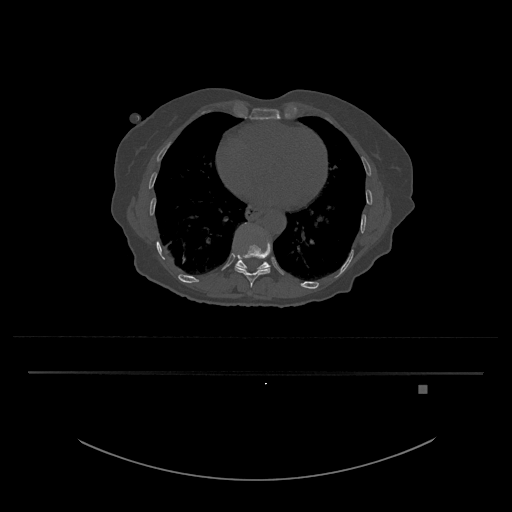
CT including the spine, one axial slice; slice 698 of 797 in the series (ordered by position); reconstruction kernel Br40s/3; bone window (W 1800 / L 400 HU); 0.5 mm slice thickness; 512 × 512 image matrix, field of view 500 × 500 mm. Patient: female, 57 years. Case-level facts recorded for this patient, not image findings: primary cancer: cervical.
Outlined on this slice (semi-automatic segmentation, software-assisted and operator-edited):
- T10 vertebra: bounding box (x1, y1, x2, y2) in pixels: (235, 244, 271, 288)
- T11 vertebra: (233, 223, 271, 269)